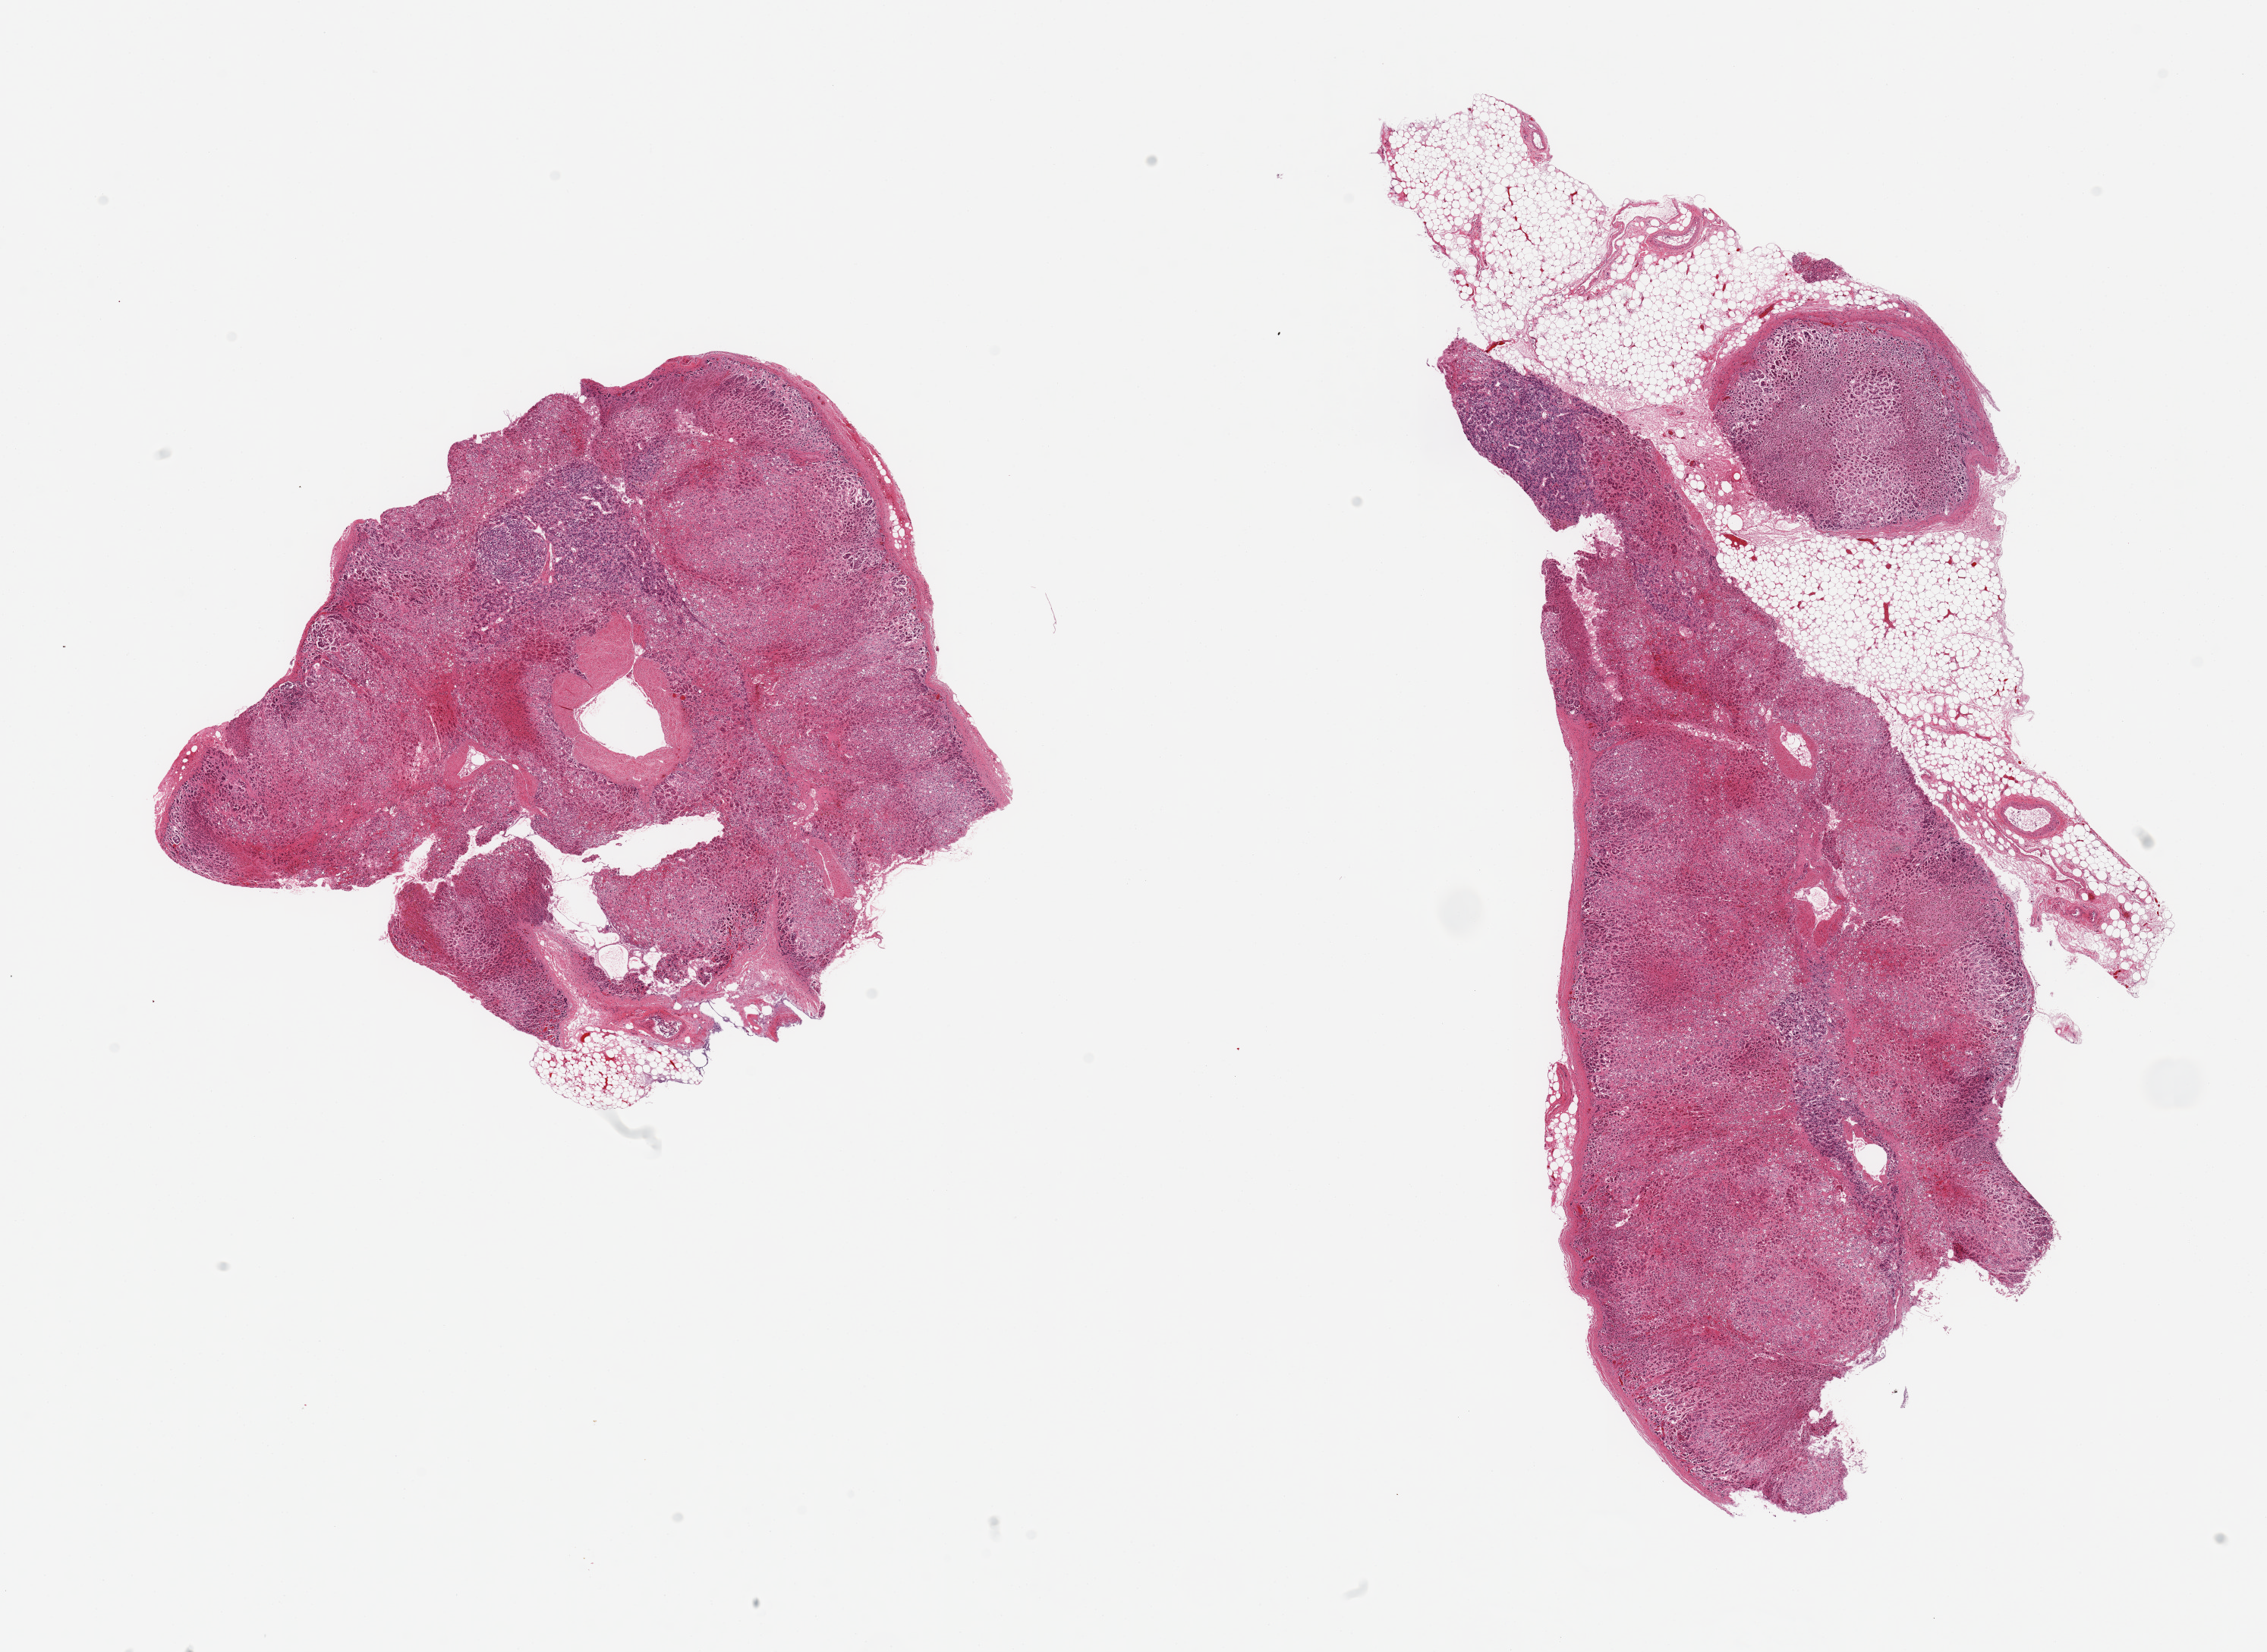
H&E whole-slide image — shown as a low-resolution overview of the whole scanned area (about 23.6 x 17.2 mm, from a 20x scan); PAXgene-fixed paraffin-embedded (PFPE) section; section of adrenal gland (target tissue); donor tissue sample. Donor sex: male.
Reviewer comment on this tissue sample: 2 pieces, ~20% adherent fat, possible focal medulla, but advanced autolysis is present.